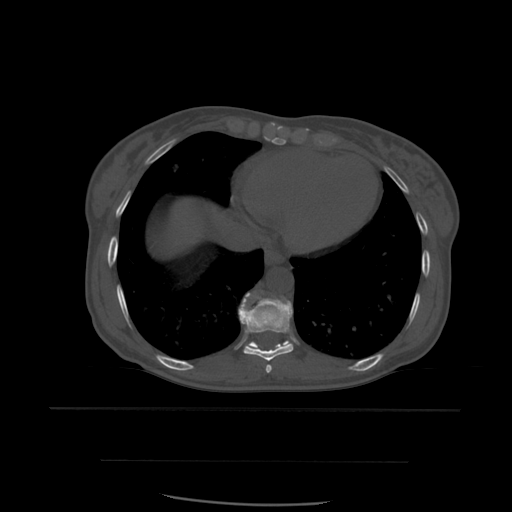
CT including the spine, one axial slice; slice 332 of 574 in the series (ordered by position); bone window (W 1800 / L 400 HU); 1.25 mm slice thickness; 512 × 512 image matrix, field of view 392 × 392 mm. Patient age 48 years. Case-level facts recorded for this patient, not image findings: primary cancer: lung; vertebrae with lytic lesions (as recorded): T11.
Outlined on this slice (semi-automatically segmented with operator editing):
- T10 vertebra: bounding box (x1, y1, x2, y2) in pixels: (250, 341, 288, 347)
- T8 vertebra: (266, 365, 273, 373)
- T9 vertebra: (239, 293, 294, 361)